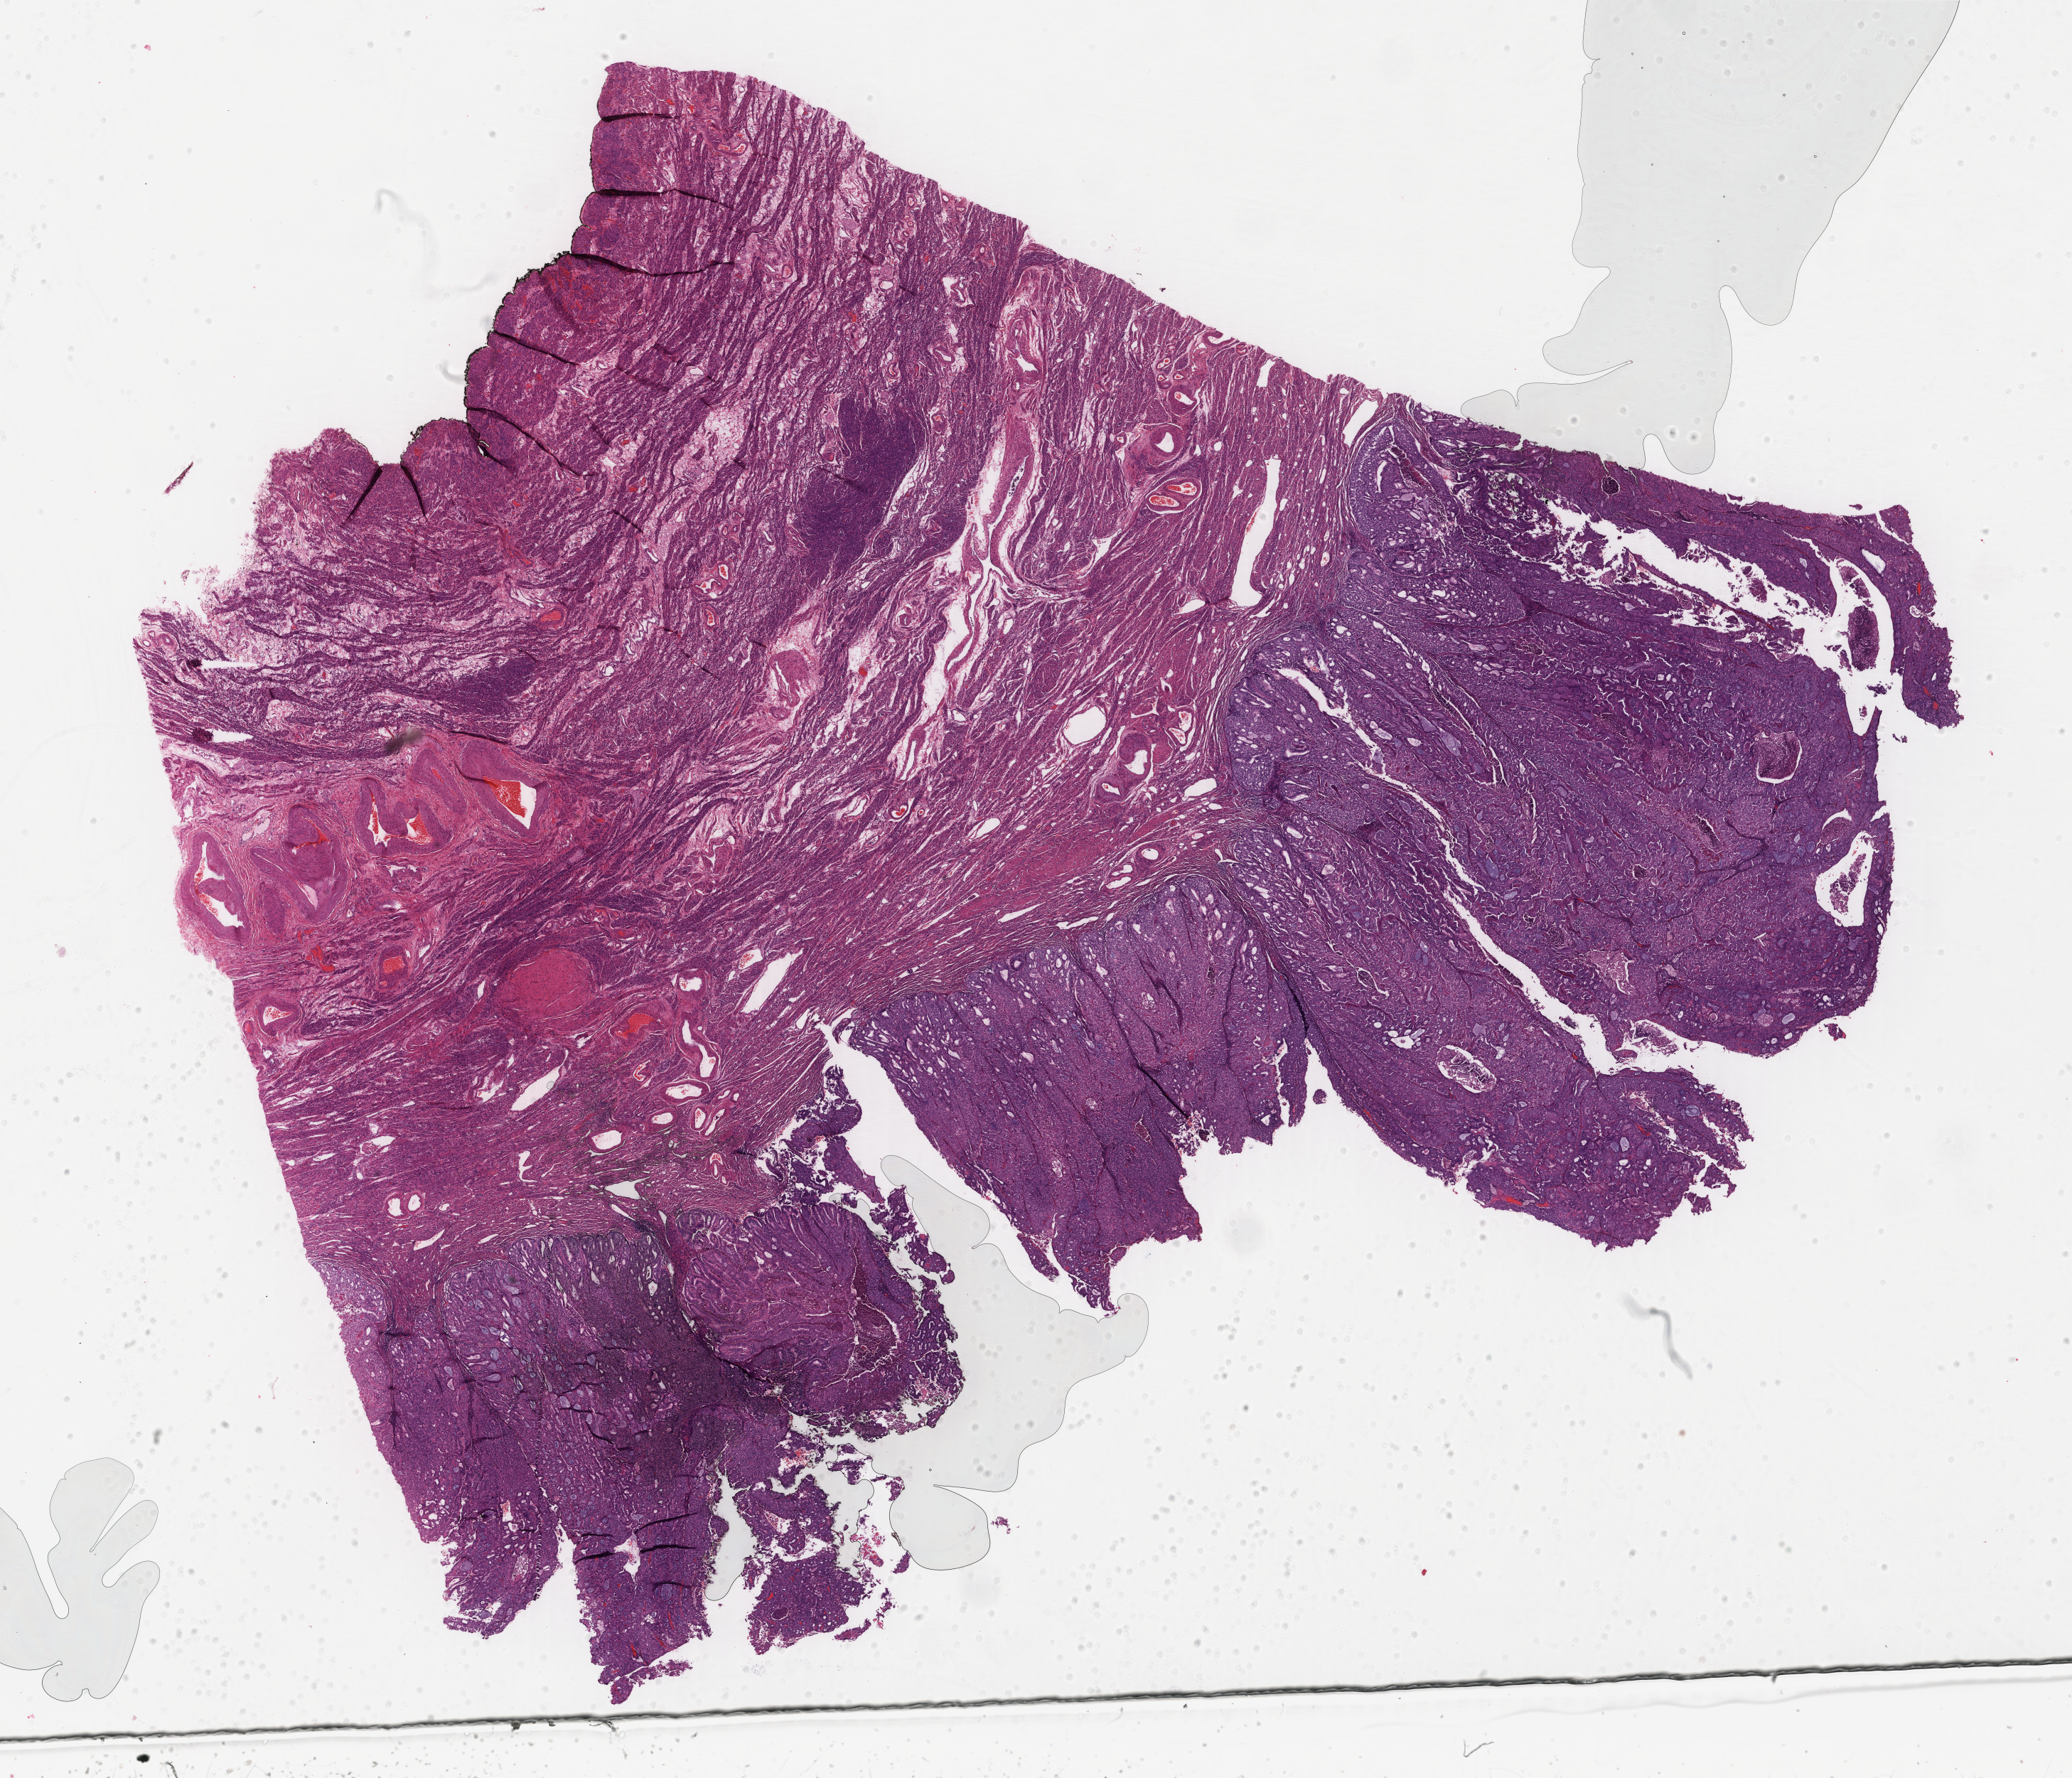
H&E whole-slide image, low-resolution overview of the scanned area, about 23.1 x 19.9 mm (slide scanned at 40x). Formalin-fixed paraffin-embedded (FFPE) diagnostic section. Primary tumour sample from the uterus. Female, age 74 years at initial diagnosis. Histologic grade: G3 (poorly differentiated).
- FIGO stage: IA
- diagnosis: Endometrioid adenocarcinoma, NOS (endometrium)